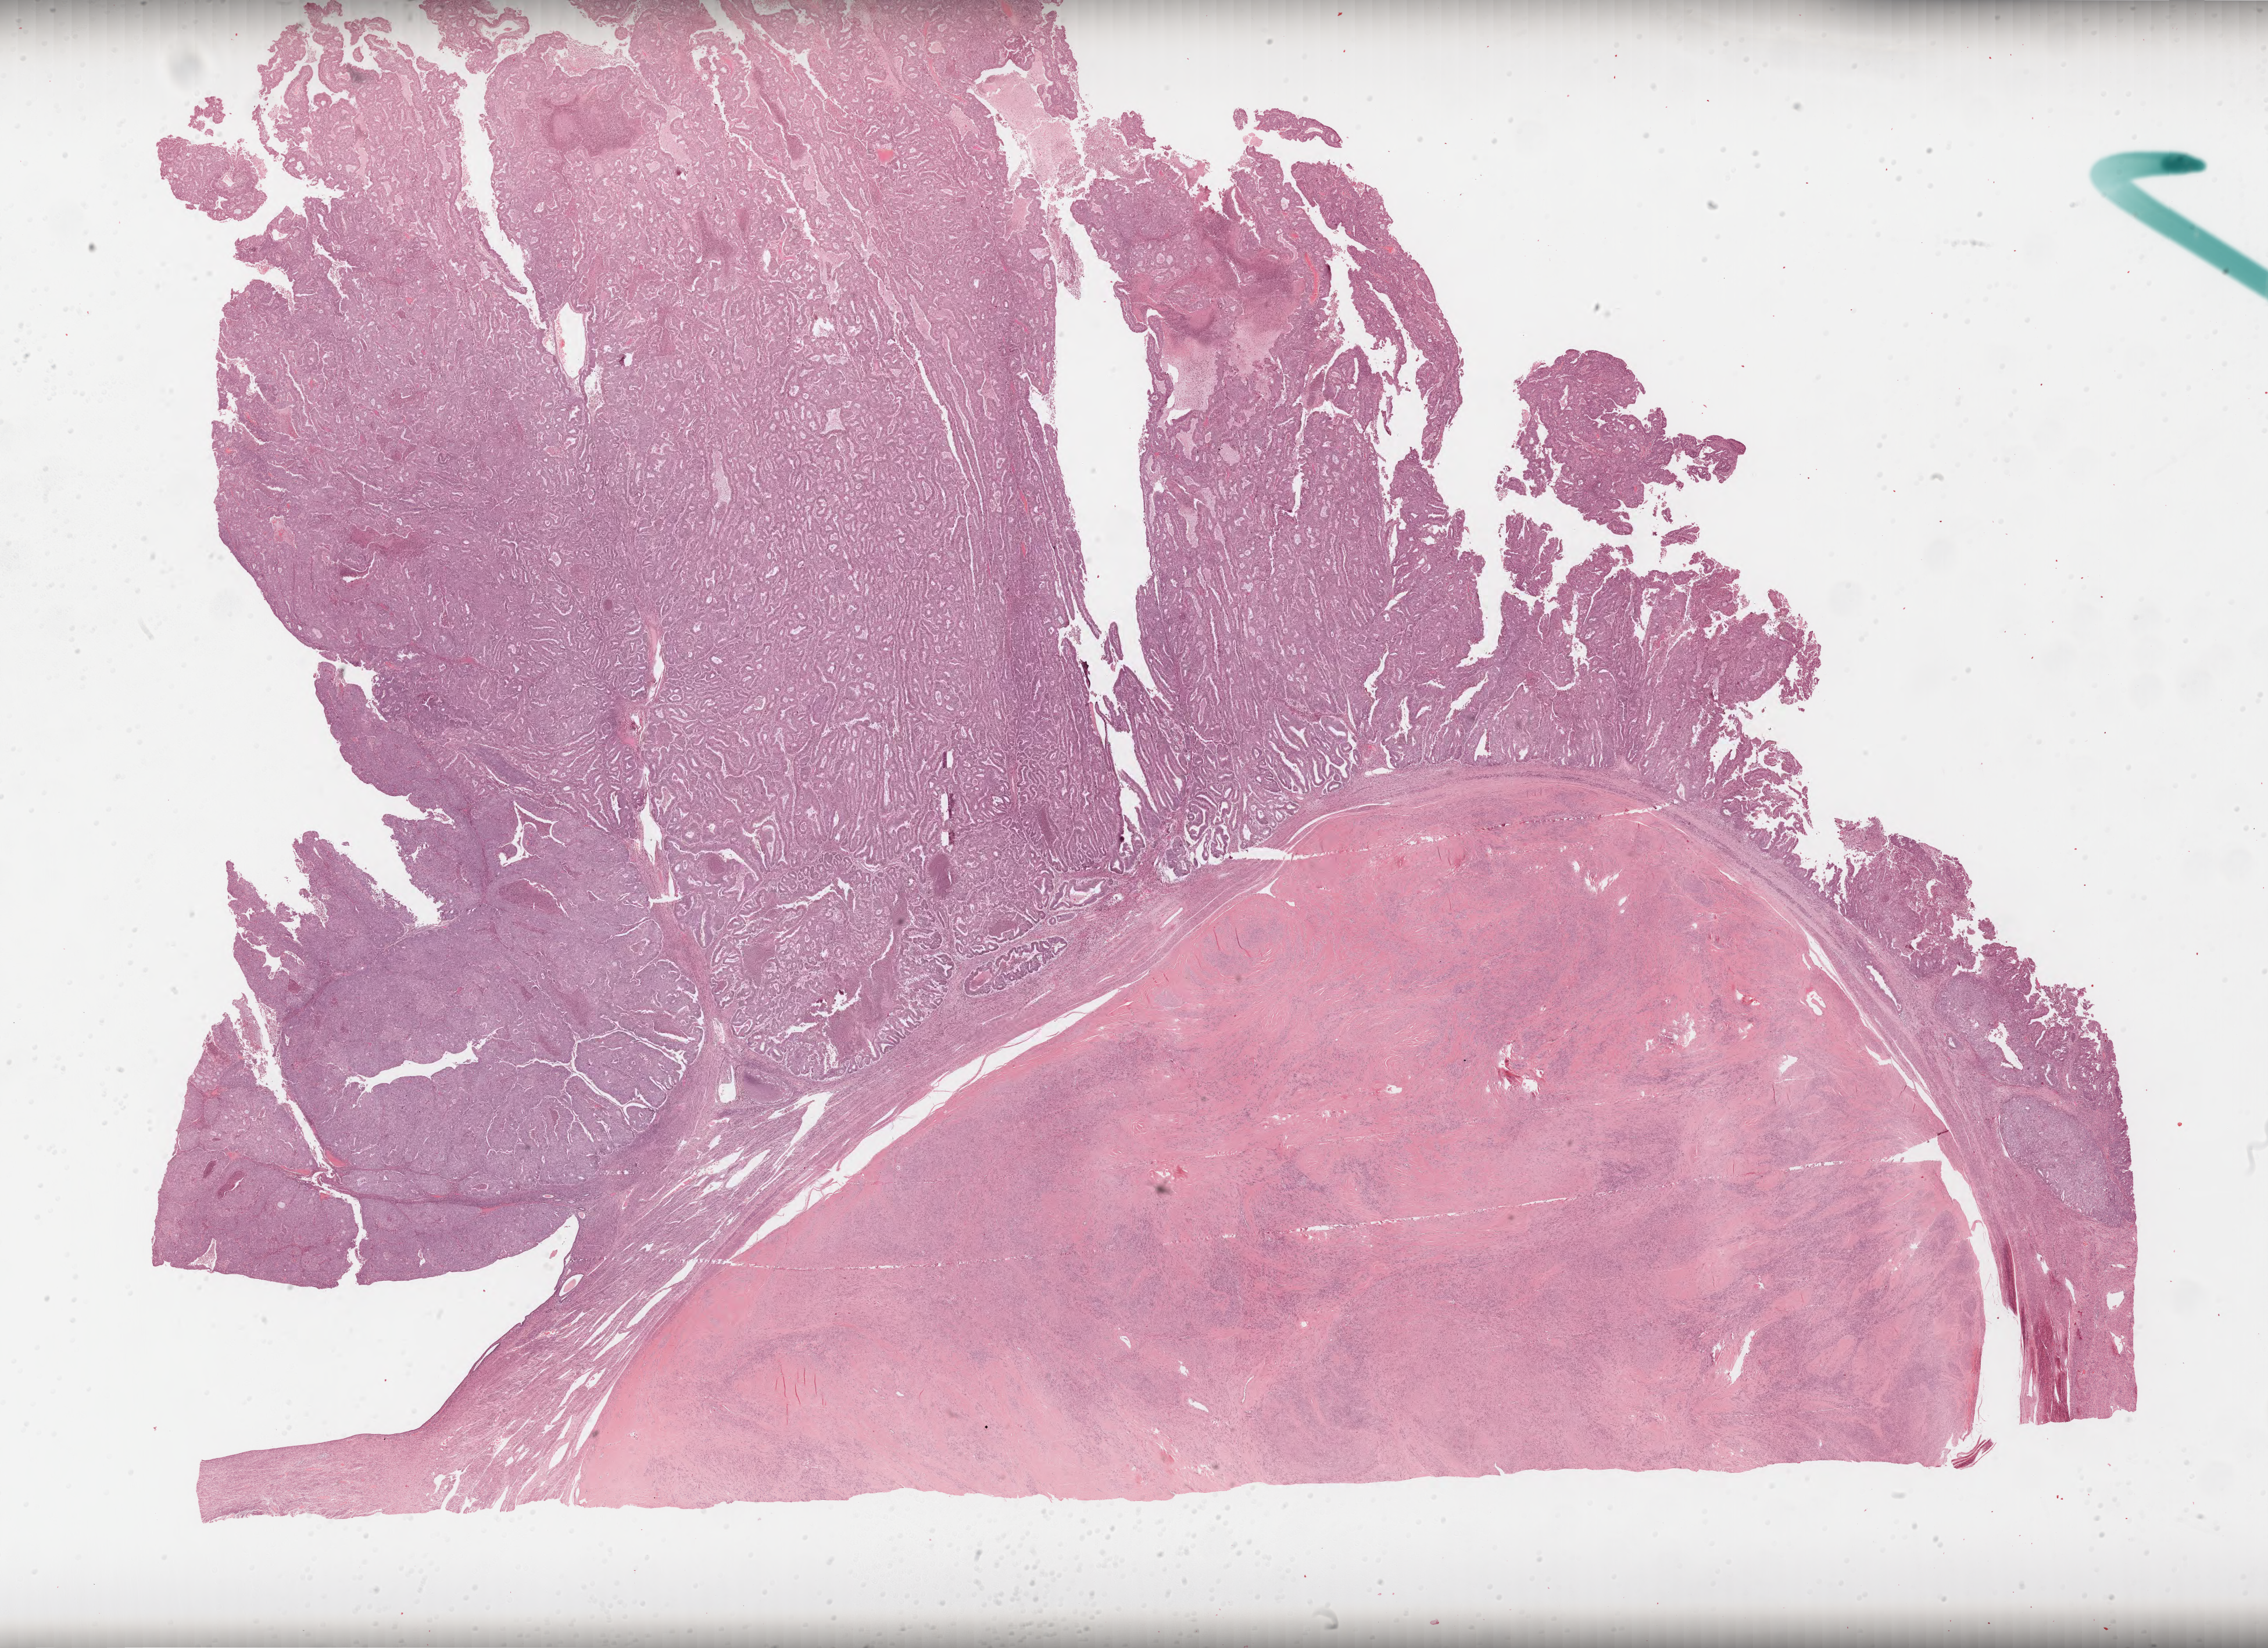
Digitized Hematoxylin and eosin (H&E) stained tissue section (whole slide) — shown as a low-resolution overview of the whole scanned area (about 31.4 x 22.8 mm); formalin-fixed paraffin-embedded (FFPE) diagnostic section; sample: primary tumour, uterus. Patient: female, age at initial diagnosis 76 years. Histologic grade: G3 (poorly differentiated).
FIGO stage: IA. Pathologic diagnosis: Endometrioid adenocarcinoma, NOS (endometrium).